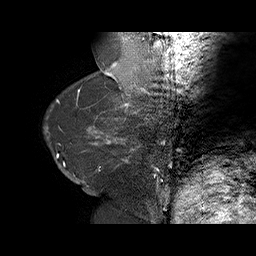
Breast MRI (dynamic contrast-enhanced), one sagittal slice; dynamic contrast-enhanced series, time point 2 of 6 at this slice position (early post-contrast); 1.5 T; TE 4.5 ms, TR 32.4 ms; 3 mm slice thickness; 256 × 256 image matrix, field of view 180 × 180 mm. Female patient. From the clinical record (not read from this slice): setting: breast cancer imaged before/during neoadjuvant chemotherapy; receptor status: HR-positive, HER2-negative.
Annotated regions visible in this slice (semi-automatically segmented with operator editing):
- analysis volume of interest (the breast-tissue region the enhancement analysis was run in; not a lesion): bounding box <58,134,166,191> (left, top, right, bottom; pixels)
- tumour enhancement mask (voxels above the 100 % enhancement threshold inside the analysis volume of interest): <58,138,158,190>